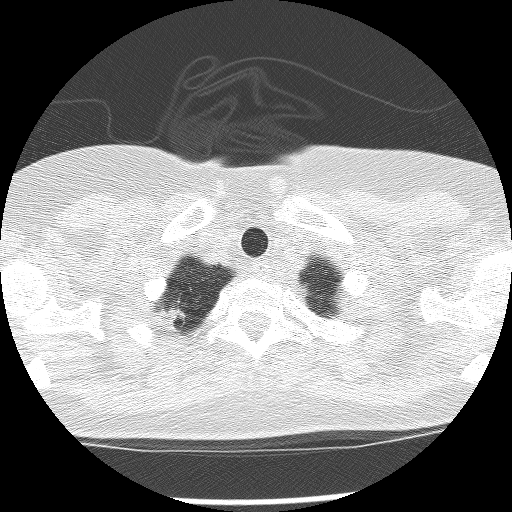
Axial slice from a low-dose chest CT screening exam, baseline screening round, lung window (W 1500 / L -600 HU), lung (sharp) reconstruction kernel (BONE), 120 kVp. Female, age 56 years at enrolment.
Expert-annotated lung lesion, bounding box [x1, y1, x2, y2] px = [148, 295, 196, 341]. No non-calcified nodule or mass ≥4 mm was recorded by the screening reader at this exam. Participant outcome: lung cancer diagnosed 729 days after this screen (after the third annual screen) — large cell carcinoma, NOS, right upper lobe, poorly differentiated (G3), stage IB (AJCC 6th edition), 15 mm at pathology.